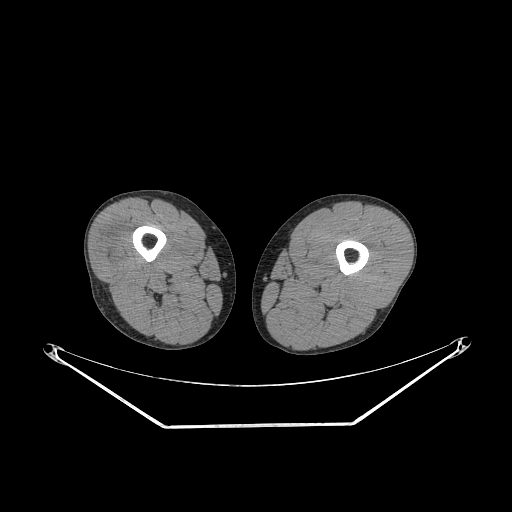
CT of an extremity soft-tissue mass (from a PET/CT study), one axial slice. Position 218 of 267 along the scan axis. Soft-tissue window (W 400 / L 40 HU). 3.75 mm slice thickness. 512 × 512 image matrix. Male patient. Case-level facts recorded for this patient, not image findings: histological type: poorly differentiated synovial sarcoma; grade: high; site of the primary tumour: right buttock.
Outlined on this slice (expert contour drawn on MRI and transferred to this co-registered scan by the dataset authors):
- gross tumour volume including surrounding oedema: bounding box [x1, y1, x2, y2] px = [105, 237, 133, 268]